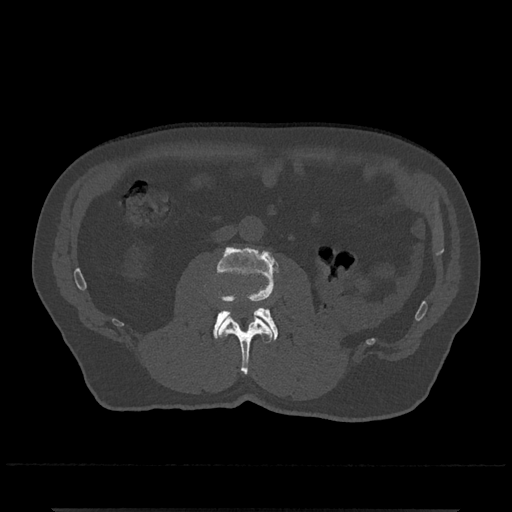
CT including the spine, one axial slice. 120 kVp. Bone window (W 1800 / L 400 HU). 0.5 mm slice thickness. 512 × 512 image matrix, field of view 393 × 393 mm. Male patient, age 67 years. From the clinical record (not read from this slice): primary cancer: prostate.
Annotated regions visible in this slice (semi-automatic segmentation, software-assisted and operator-edited):
- L2 vertebra: bounding box [x1, y1, x2, y2] px = [219, 315, 273, 374]
- L3 vertebra: [213, 247, 278, 341]